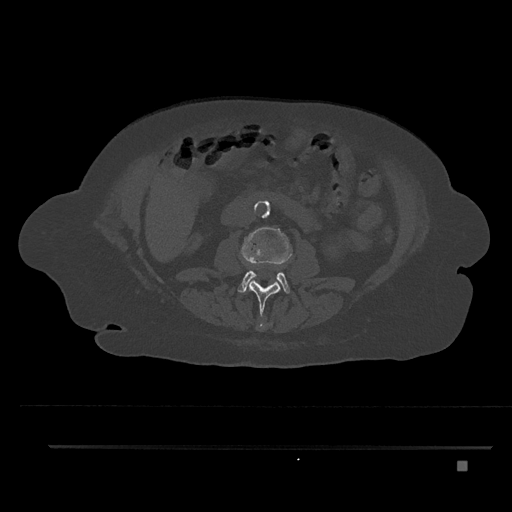
CT including the spine, one axial slice. Position 155 of 797 along the scan axis. 120 kVp. Bone window (W 1800 / L 400 HU). 512 × 512 image matrix. Patient: female, 76 years. From the clinical record (not read from this slice): primary cancer: lung; vertebrae with lytic lesions (as recorded): T11, L3.
Outlined on this slice (semi-automatically segmented with operator editing):
- L1 vertebra: bounding box [x1, y1, x2, y2] px = [259, 322, 268, 328]
- L2 vertebra: [246, 280, 280, 328]
- L3 vertebra: [238, 227, 293, 293]